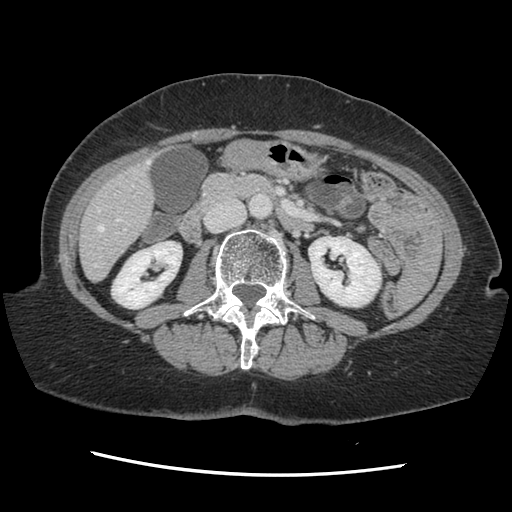
Contrast-enhanced abdominal CT, one axial slice. Position 48 of 141 along the scan axis. Soft-tissue window (W 400 / L 40 HU). 2.5 mm slice thickness. 512 × 512 image matrix, field of view 330 × 330 mm. Female patient, age 61 years. Case-level facts recorded for this patient, not image findings: diagnosis: colorectal cancer liver metastases, imaged before liver resection; multiple liver metastases: no; largest metastasis: 2.4 cm; disease in both lobes: no.
Structures marked on this image (outlined manually by an expert reader):
- hepatic veins: bounding box [x1, y1, x2, y2] px = [94, 161, 149, 266]
- liver: [81, 162, 154, 280]
- planned liver remnant (the part of the liver to remain after resection): [81, 188, 154, 280]
- portal vein (with intrahepatic branches): [98, 229, 126, 250]